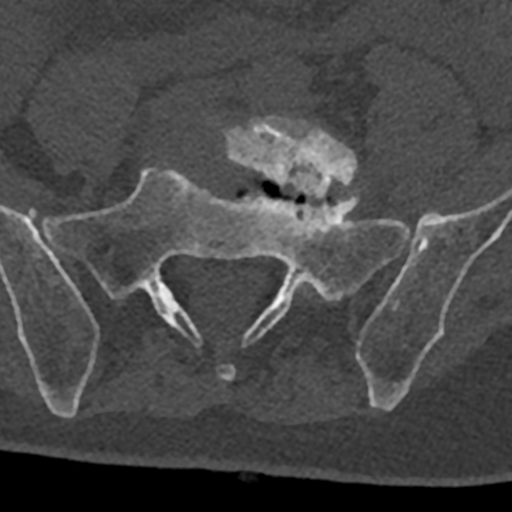
CT including the spine, one axial slice. Bone window (W 1800 / L 400 HU). 0.5 mm slice thickness. 512 × 512 image matrix. Patient: male, 74 years. Case-level facts recorded for this patient, not image findings: primary cancer: renal.
Annotated regions visible in this slice (semi-automatic segmentation, software-assisted and operator-edited):
- L5 vertebra: box from (x=219, y=115) to (x=357, y=199) px